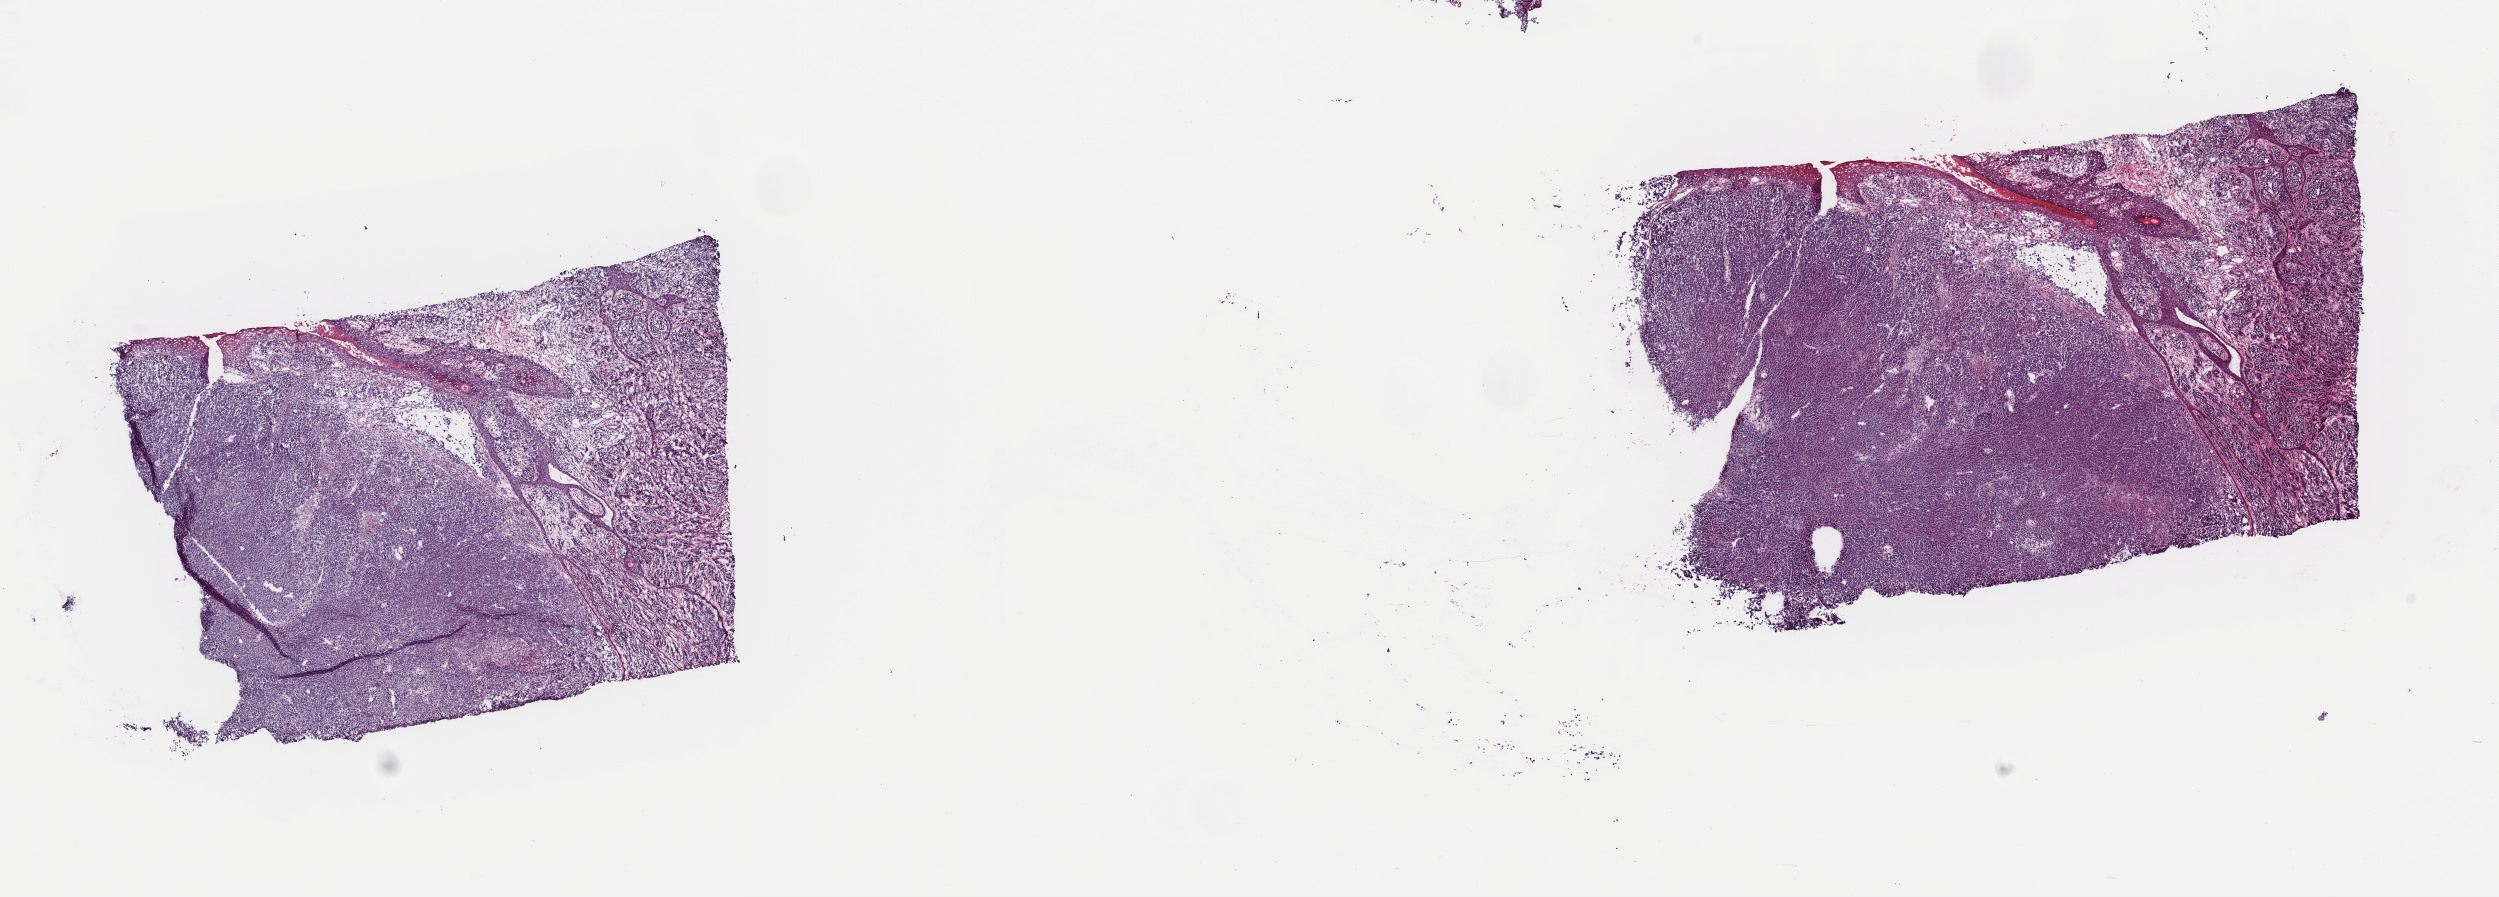
Digitized H&E-stained tissue section (whole slide), low-resolution overview of the scanned area, about 19.7 x 7.1 mm (from a 40x scan), frozen section from the top of the tissue portion, primary tumour sample from the skin. Female patient; age at initial diagnosis 36 years. Composition of this section per pathologist review: tumour cells 75%, tumour nuclei 70%, normal cells 5%, stromal cells 20%, necrosis 0%. Inflammatory infiltration, as recorded: lymphocyte infiltration 0%, monocyte infiltration 0%, neutrophil infiltration 0%.
TNM: T4b N1 M0. Histologic diagnosis: Malignant melanoma, NOS. AJCC pathologic stage: IIIB (7th edition).